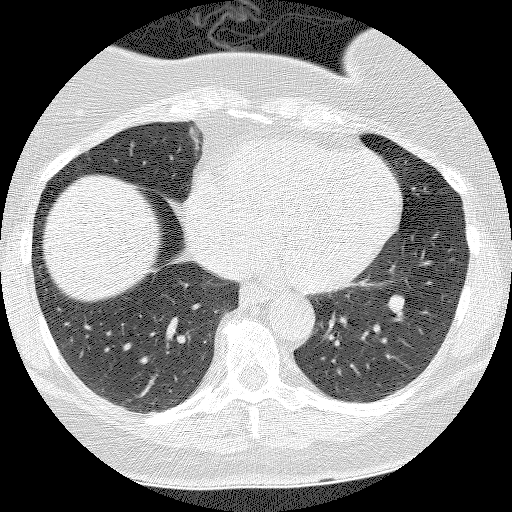
Chest CT (low-dose screening protocol), one axial image; baseline screening round; lung window (W 1500 / L -600 HU); 2.5 mm slice thickness; lung (sharp) reconstruction kernel (BONE); slice 92 of 135 in the series. Female participant, aged 55 years at enrolment.
Lesion marked by an expert reader, box from (x=372, y=286) to (x=421, y=329) px. The screening reader recorded 3 non-calcified nodules or masses ≥4 mm on this exam (left lower lobe, right lower lobe, right lower lobe); which of them this box marks is not recorded. Official screen result: positive, change unspecified: nodule(s) >= 4 mm or enlarging nodule(s), mass(es), or other non-specific abnormalities suspicious for lung cancer. Lung cancer was diagnosed 1026 days after this screen (after the third annual screen): carcinoid tumor, NOS, left lower lobe, carcinoid, stage not assessed, 10 mm at pathology.